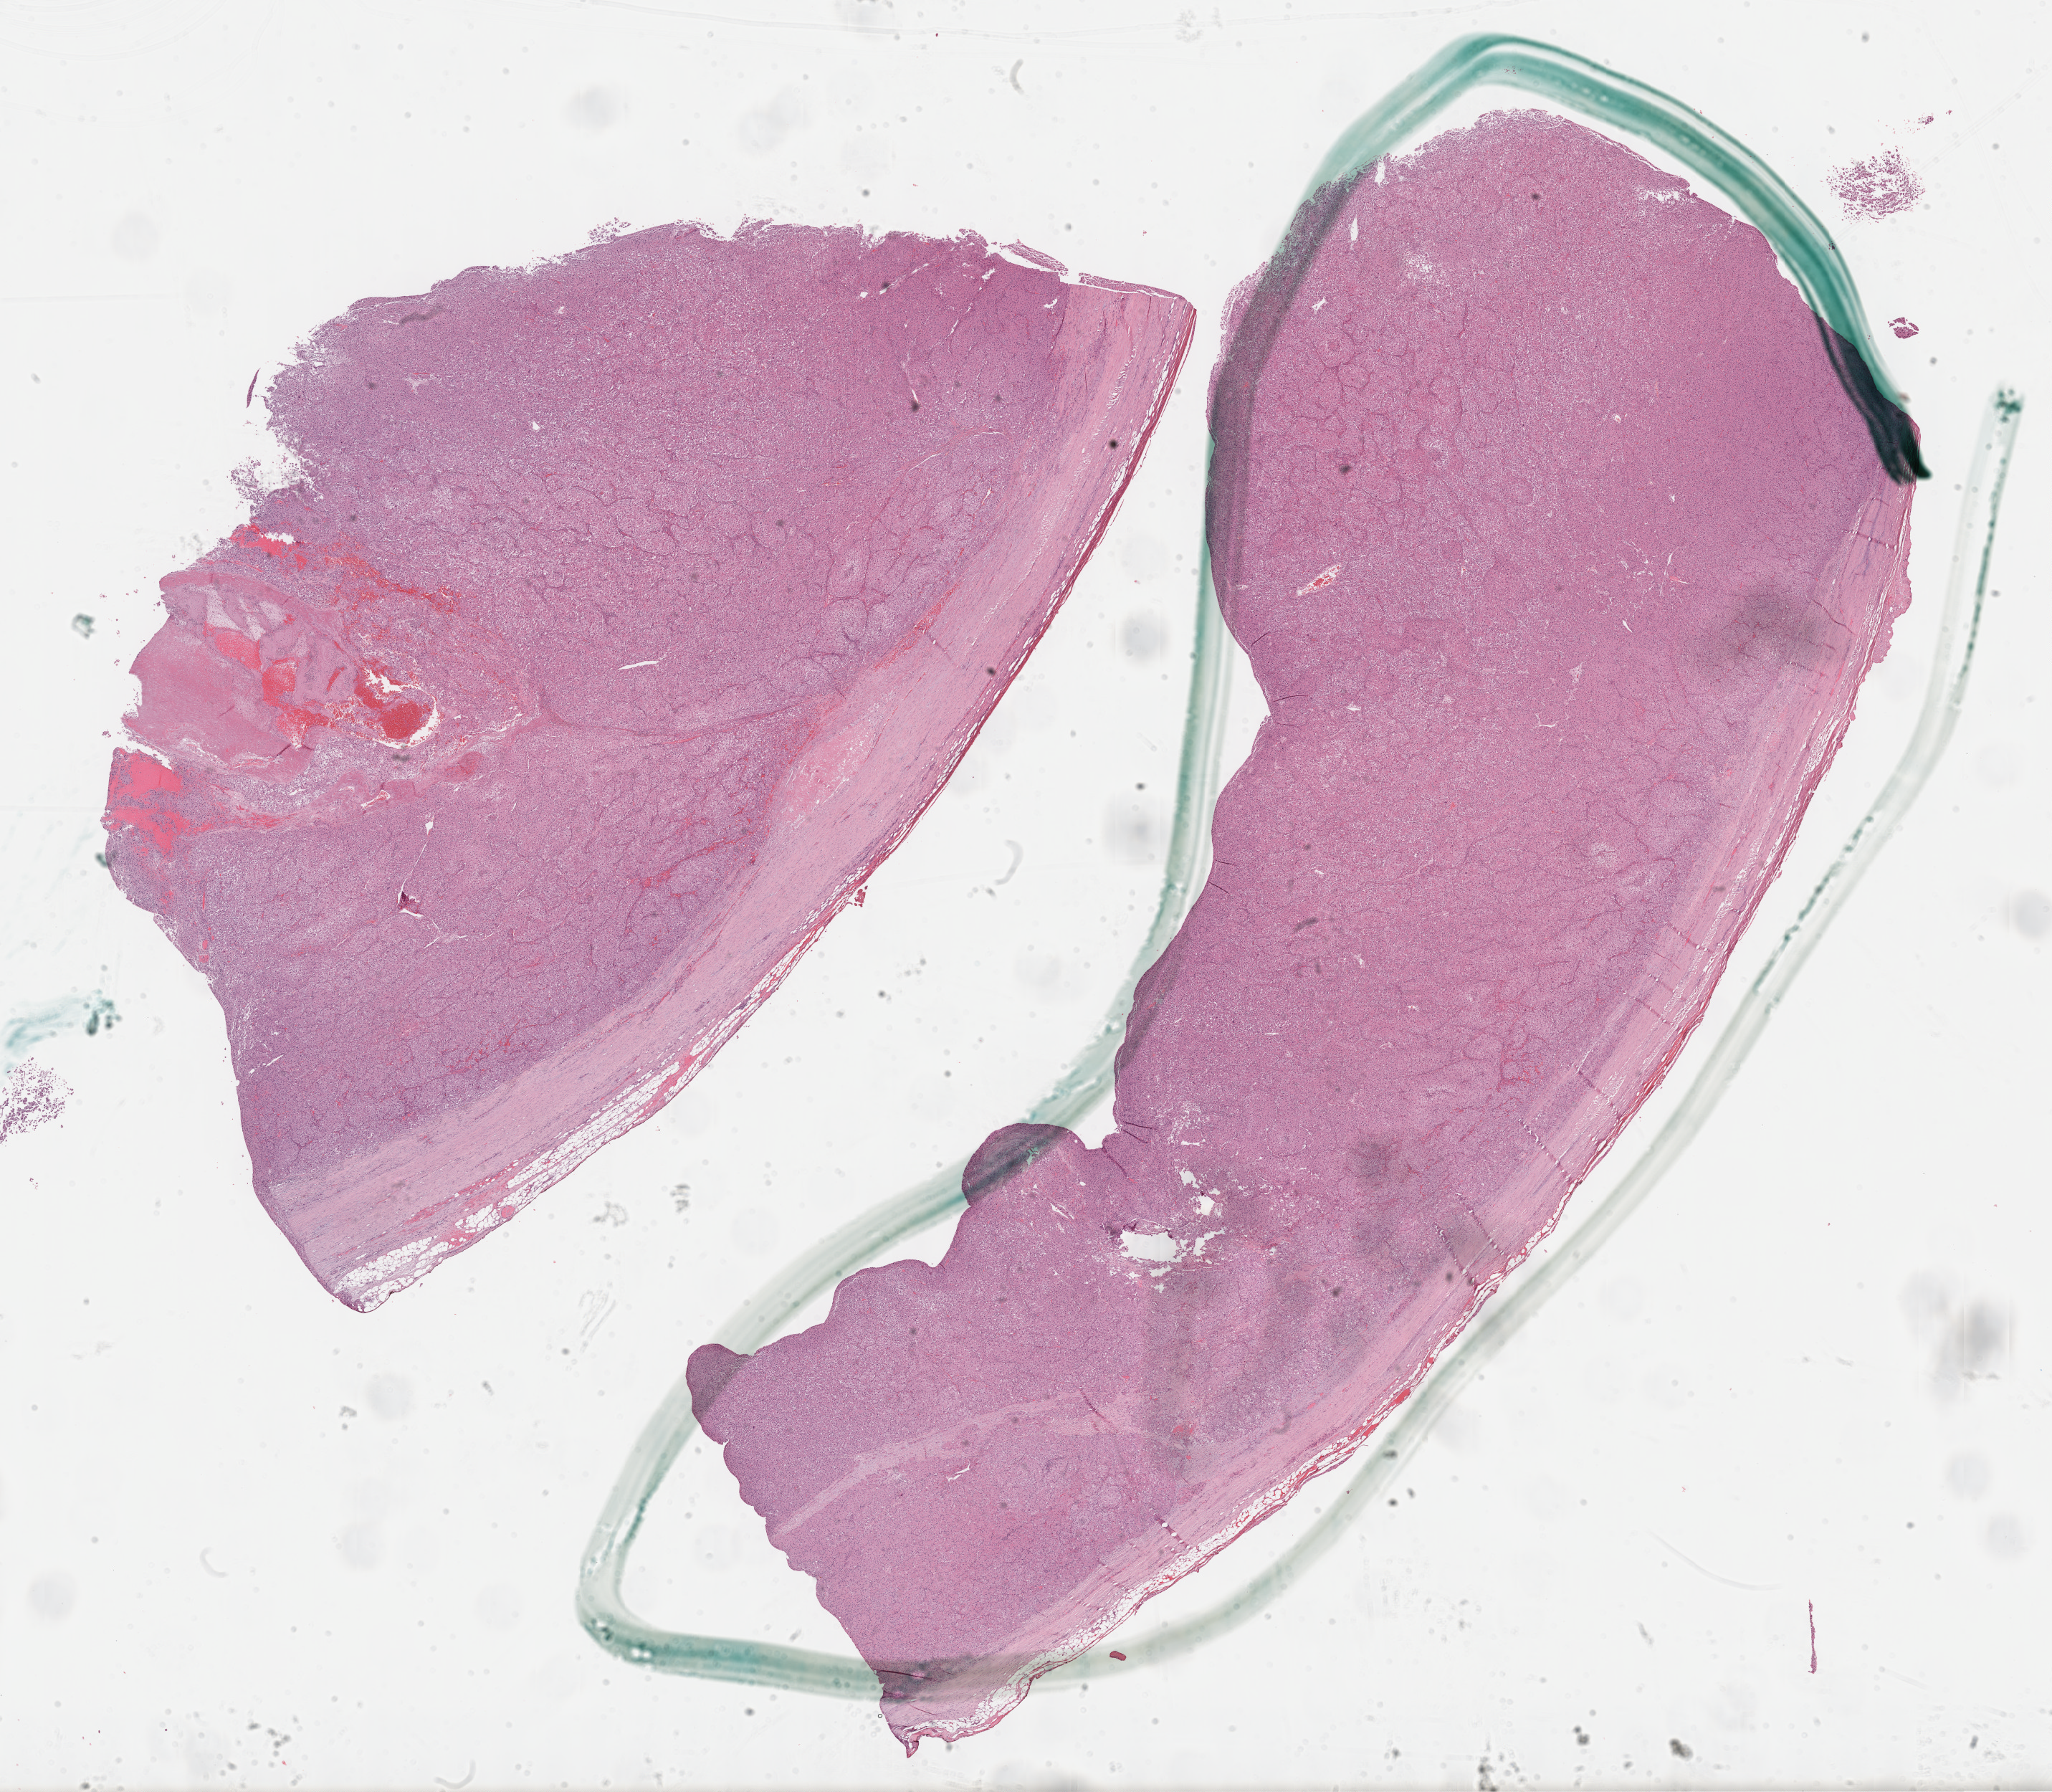
Whole-slide histology image, Hematoxylin and eosin (H&E) stained, shown as a low-resolution overview of the whole scanned area (about 23.2 x 20.2 mm, slide scanned at 40x); formalin-fixed paraffin-embedded (FFPE) diagnostic section; adrenal cortex, primary tumour sample. Male, age 55 years at initial diagnosis.
Diagnosis: Adrenal cortical carcinoma (cortex of adrenal gland).